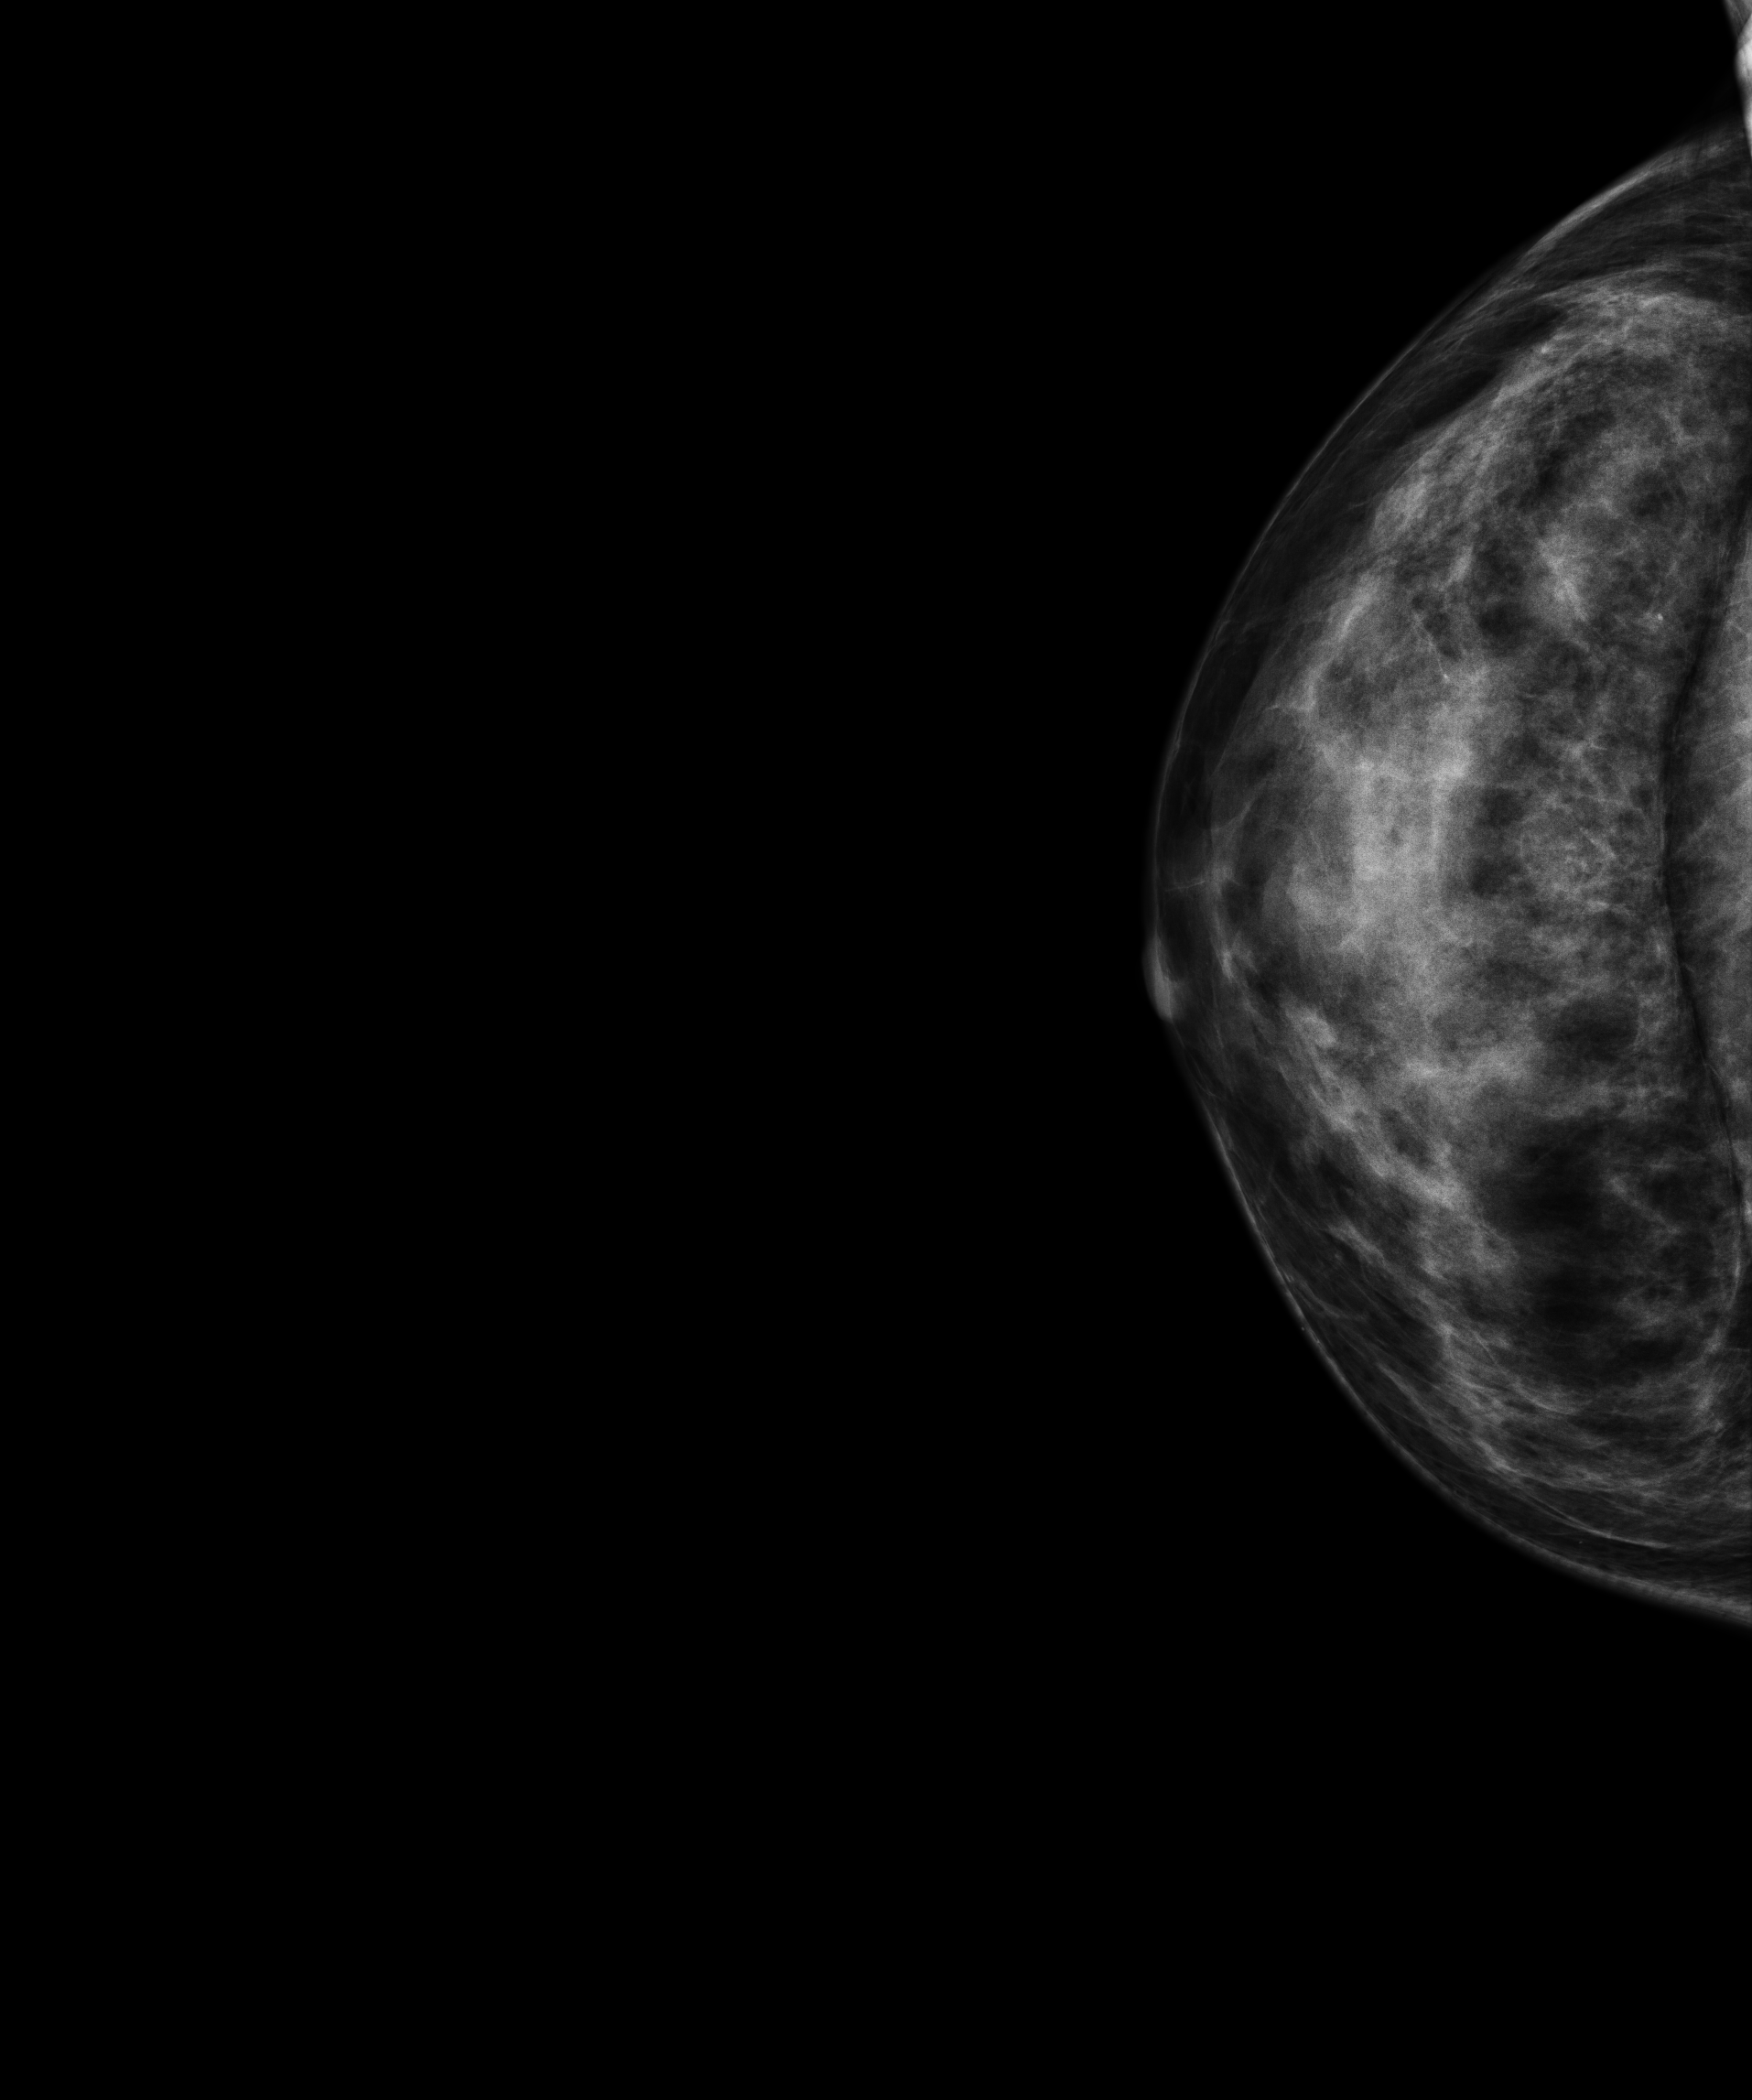
Full-field digital mammogram (FFDM); right breast; CC view; screening examination; compressed breast thickness 53 mm. Patient: female, 43 years.
BI-RADS breast density category at the screening exam (both breasts, scale 1–4): 4. Final BI-RADS assessment for this screening round (tomosynthesis exam, both breasts): category 2. Recall: no recall after this screen.